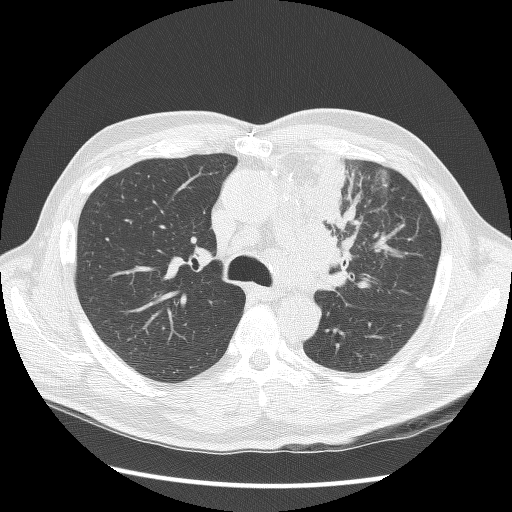
Chest CT (low-dose screening protocol), one axial image, second annual screen, lung window (W 1500 / L -600 HU), 2.5 mm slice thickness, lung (sharp) reconstruction kernel (BONE). Male participant, aged 64 years at enrolment. Former smoker at enrolment.
Expert reader's lesion annotation, box from (x=299, y=159) to (x=375, y=288) px. No non-calcified nodule or mass ≥4 mm was recorded by the screening reader at this exam. Official screen result: positive, other.